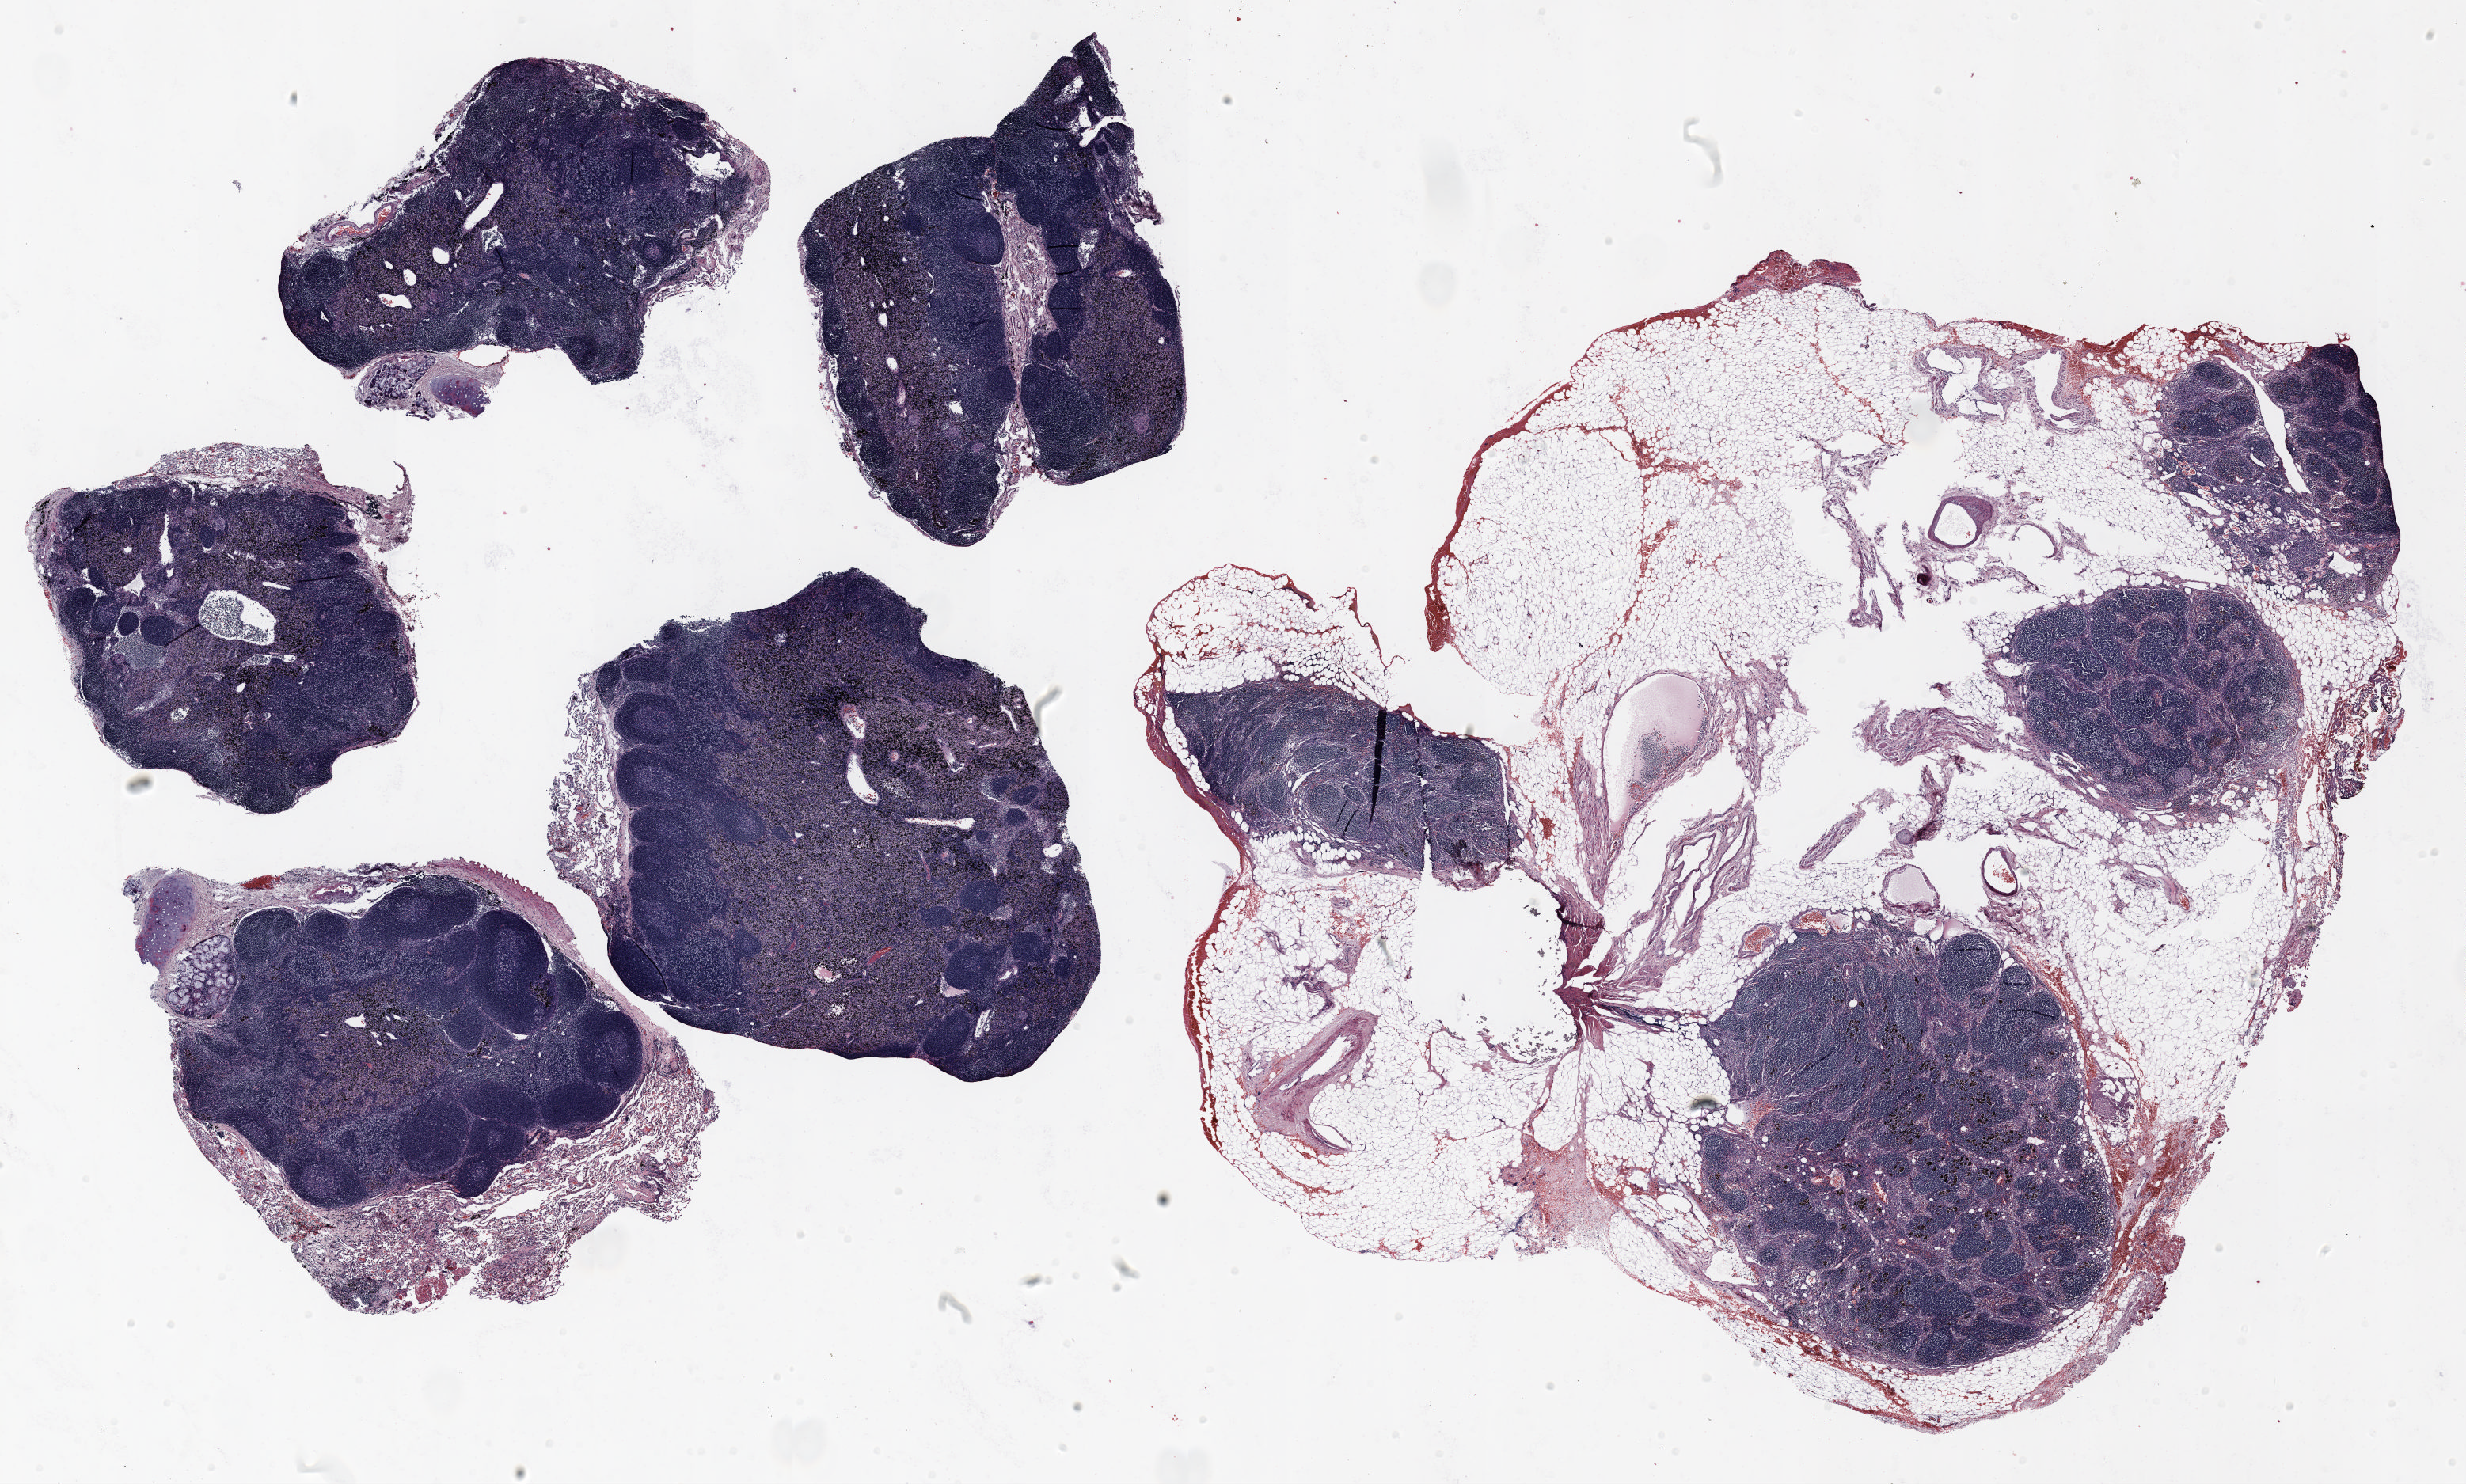
Hematoxylin and eosin (H&E) stained whole-slide image, whole scanned area (about 25.0 x 15.1 mm) shown as a low-resolution overview; FFPE section; lung. Male patient, aged 70 at enrolment. Grade: poorly differentiated (G3).
* primary tumour location (clinical record): right upper lobe
* tumour size (pathology): 23 mm
* stage (AJCC 6th edition): IIA
* participant's lung-cancer diagnosis: Adenocarcinoma, NOS